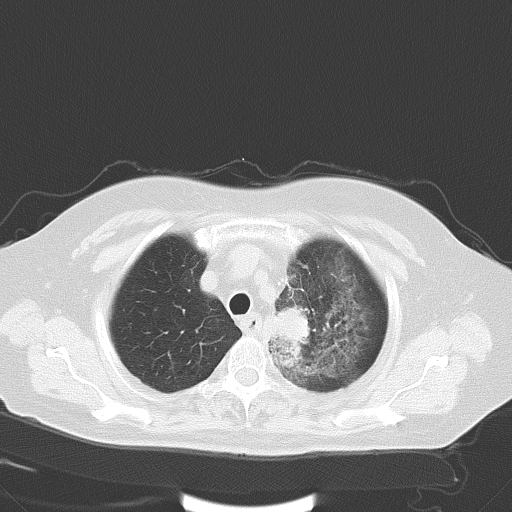
Chest CT, one axial slice; position 46 of 56 along the scan axis; 120 kVp; lung window (W 1500 / L -600 HU); 512 × 512 image matrix, field of view 353 × 353 mm. Patient: female, 65 years. From the clinical record (not read from this slice): clinical TNM (as recorded): T2b N1 M0.
Outlined on this slice (rectangle marked by the reading radiologist):
- lung tumour (recorded histology: adenocarcinoma): bounding box <273,300,319,345> (left, top, right, bottom; pixels)